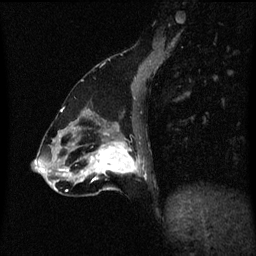
Breast MRI (dynamic contrast-enhanced), one sagittal slice. Position 23 of 60 along the scan axis. Dynamic contrast-enhanced series, image 2 of 3 at this slice position (ordered by acquisition). 1.5 T. TE 4.2 ms, TR 8.4 ms. 2 mm slice thickness. 256 × 256 image matrix. Female patient, age 47 years.
Annotated regions visible in this slice (semi-automatic segmentation, software-assisted and operator-edited):
- analysis volume of interest (the breast-tissue region the enhancement analysis was run in; not a lesion): bounding box <85,136,143,195> (left, top, right, bottom; pixels)
- tumour enhancement mask (voxels above the 70 % enhancement threshold inside the analysis volume of interest): <91,142,140,183>